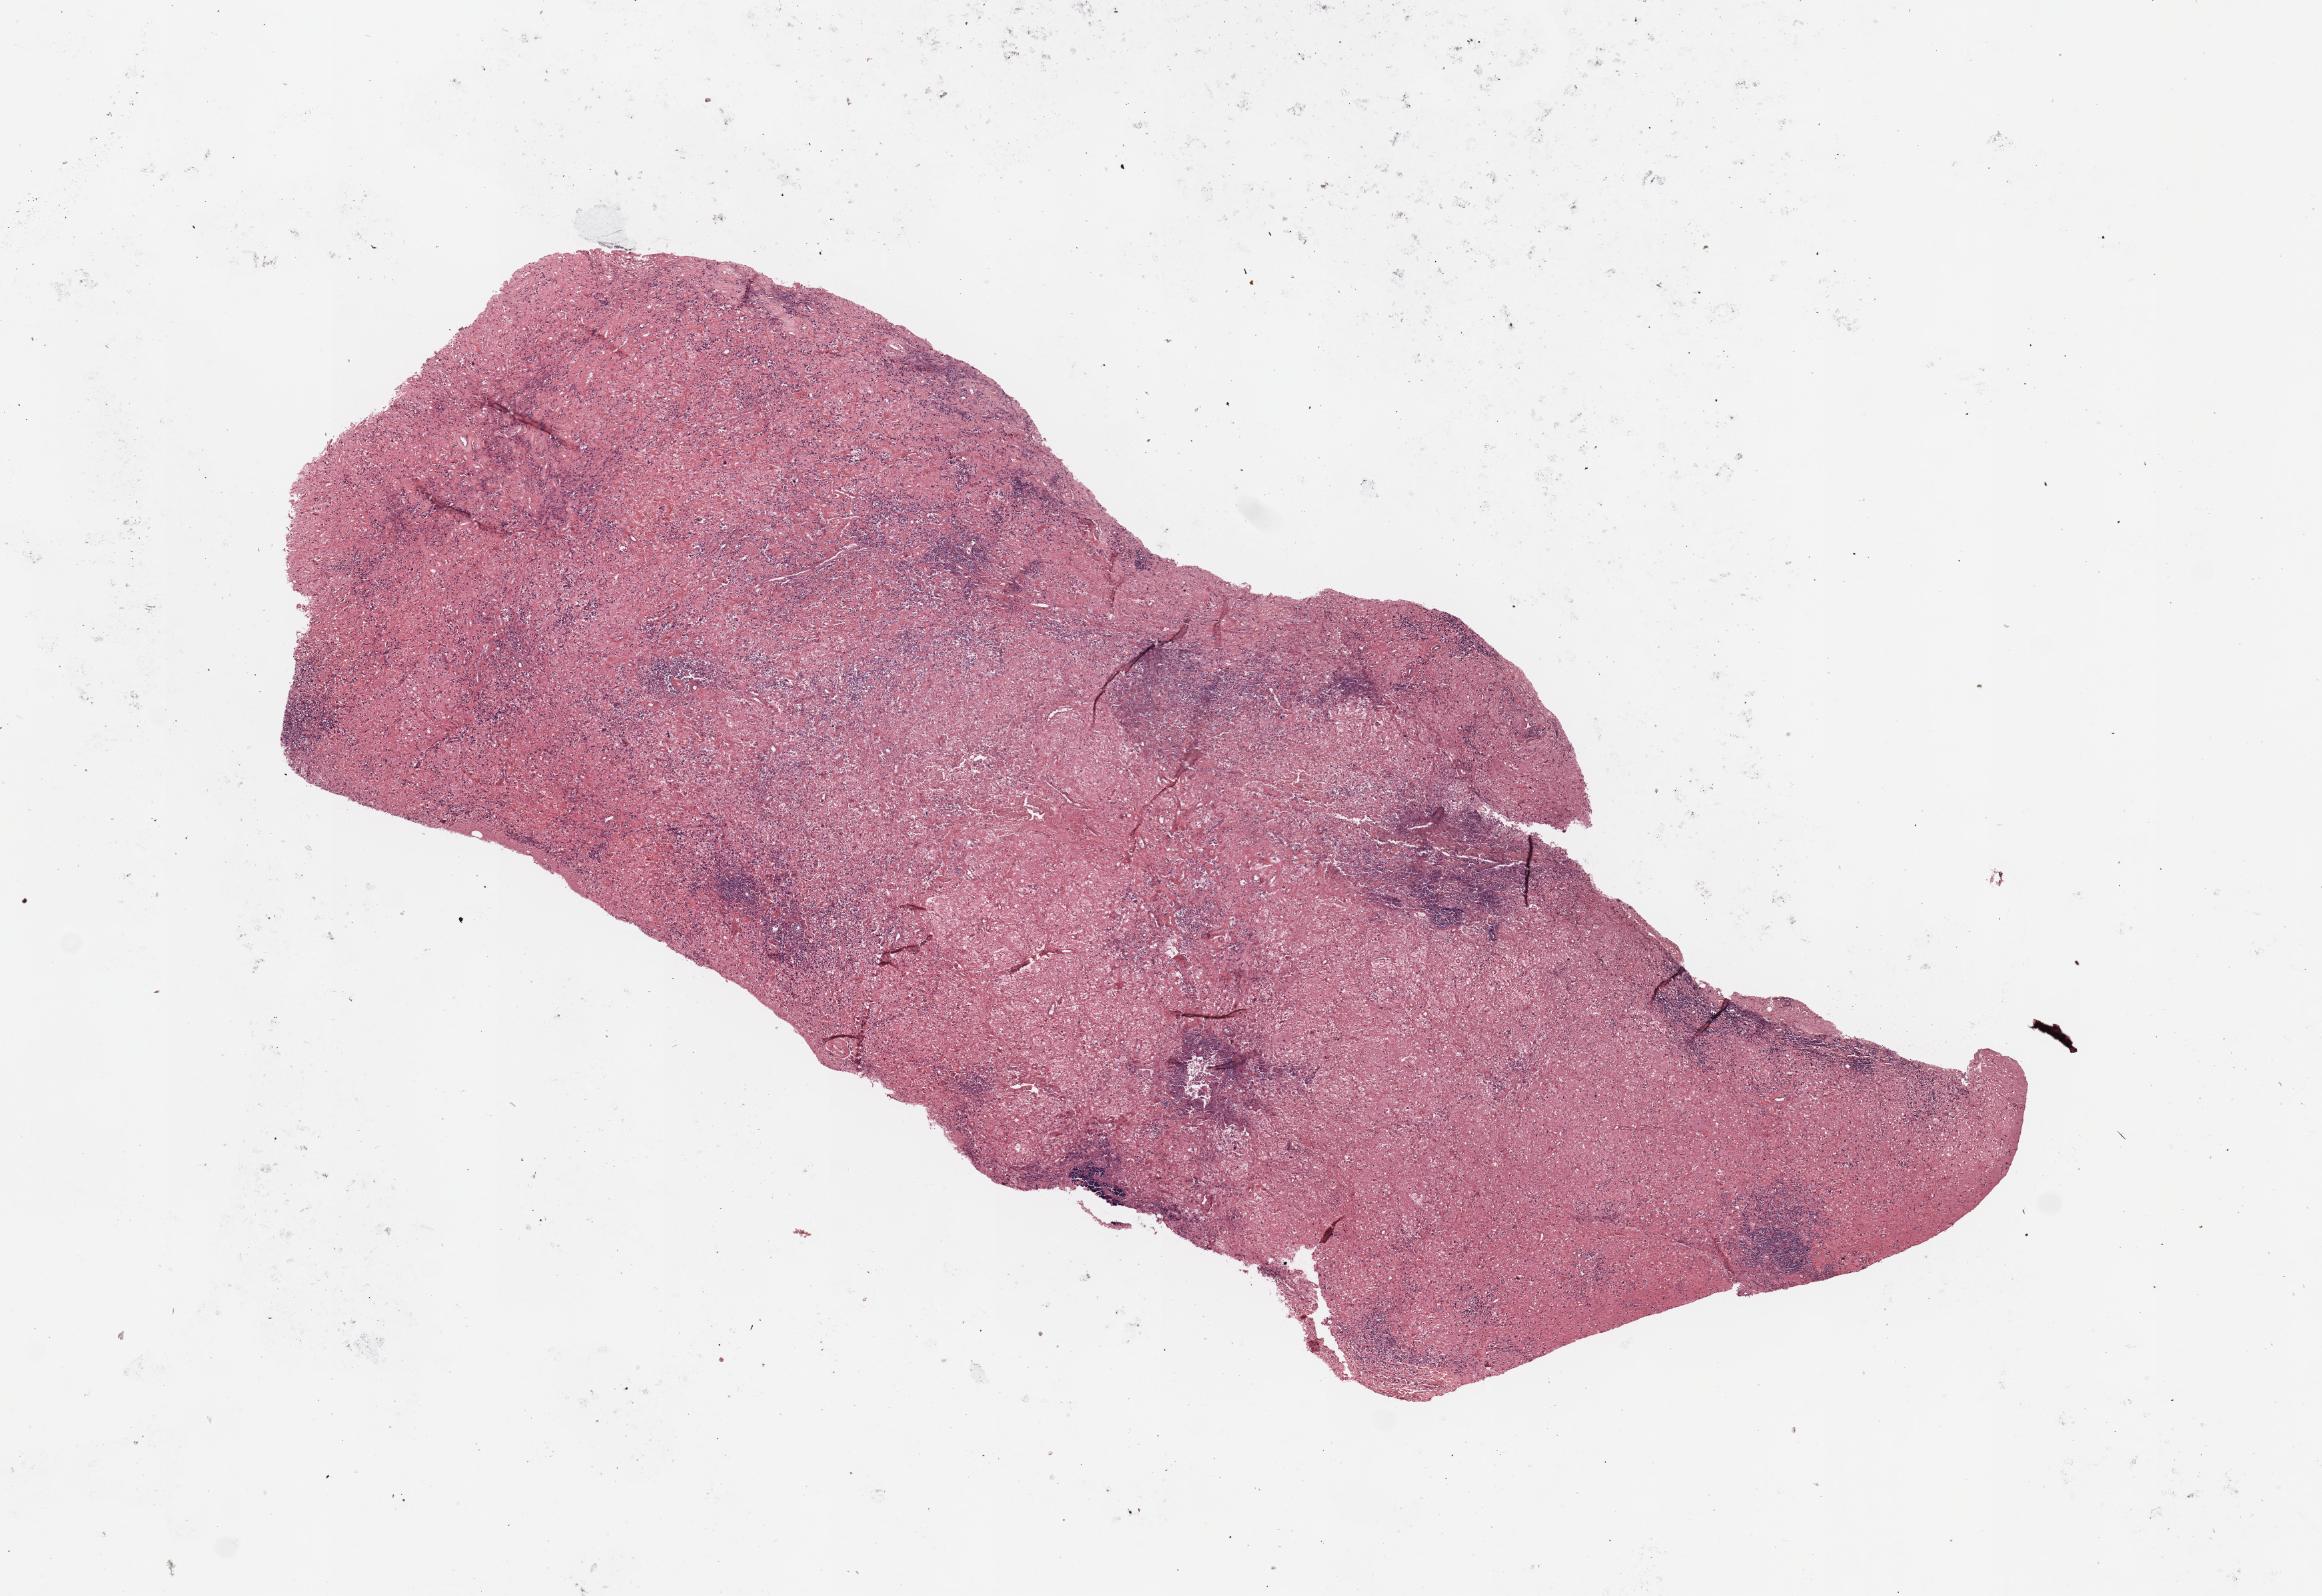
H&E-stained whole-slide image — whole scanned area (about 13.8 x 9.5 mm, from a 20x scan) shown as a low-resolution overview. Patient: male, age 64 years.
Patient diagnosis (cohort enrolment): sarcoma (site not recorded at cohort level).